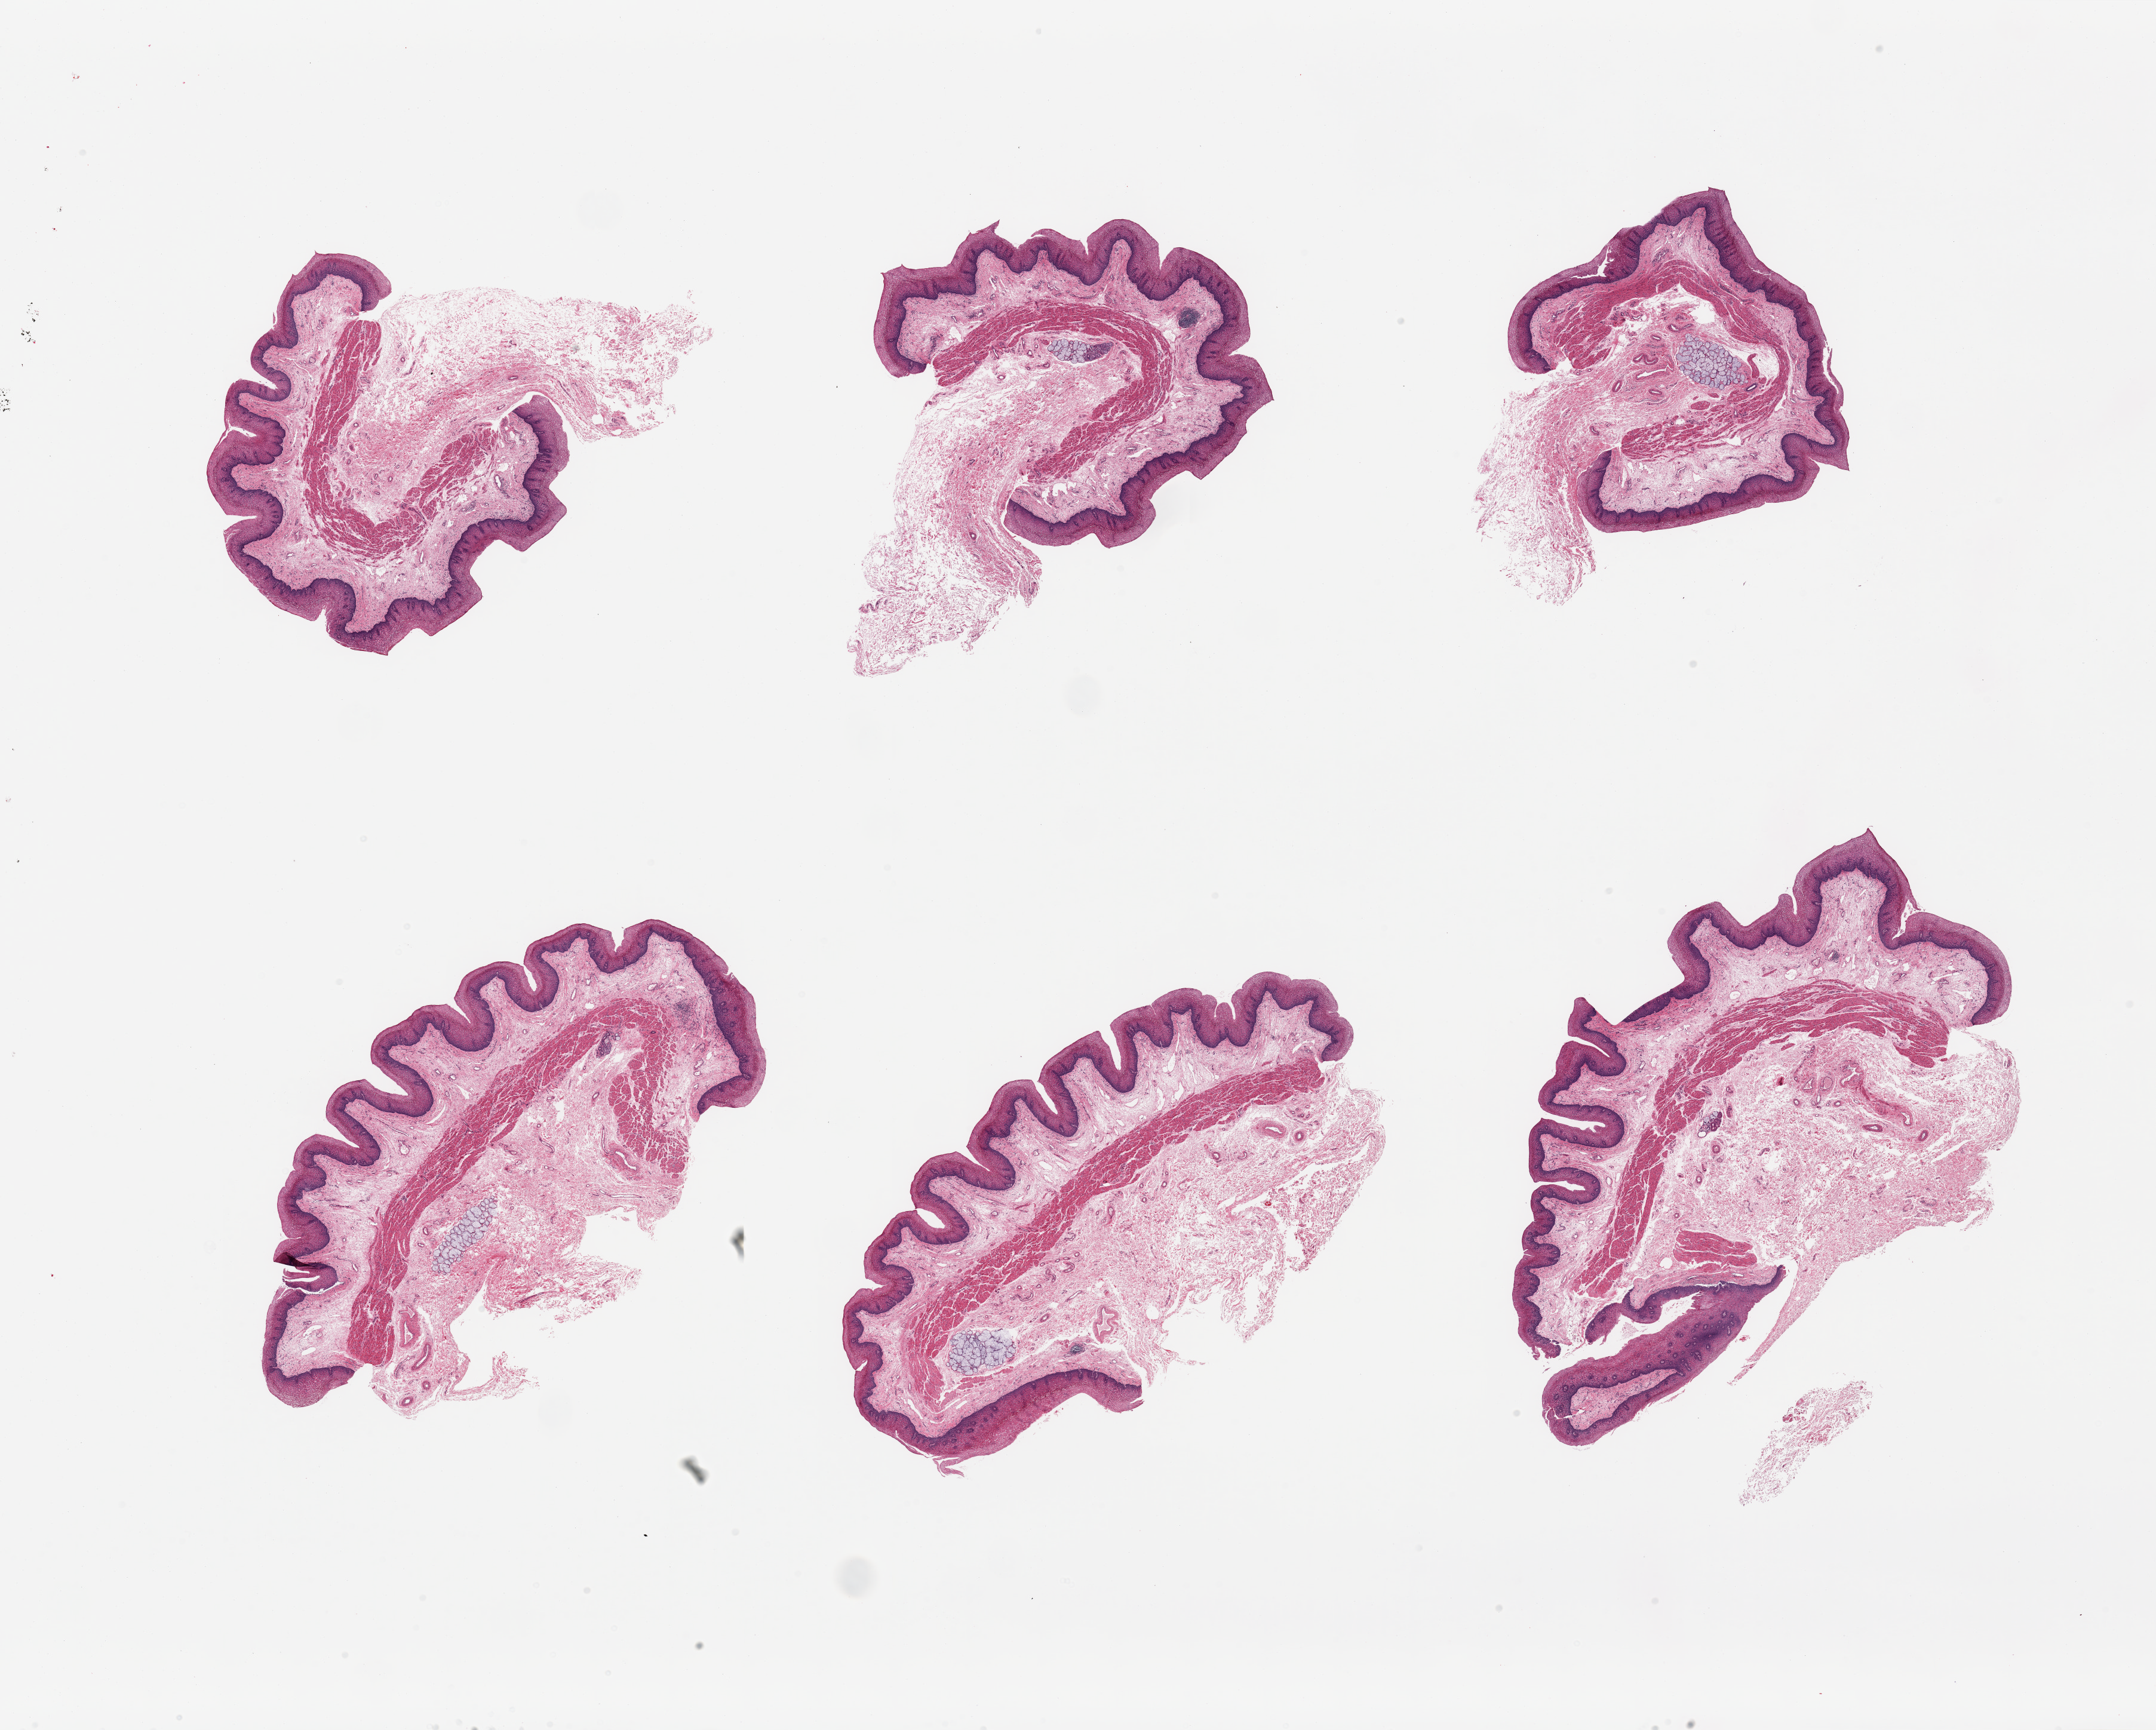
Digitized H&E-stained section, brightfield — whole scanned area (about 28.5 x 22.9 mm, slide scanned at 20x) shown as a low-resolution overview, PAXgene-fixed, paraffin-embedded tissue, target tissue: esophageal mucous membrane, tissue donor sample. Male donor.
Reviewer comment on this tissue sample: 6 pieces; well trimmed, few clusters of submucosal glands (some marked).